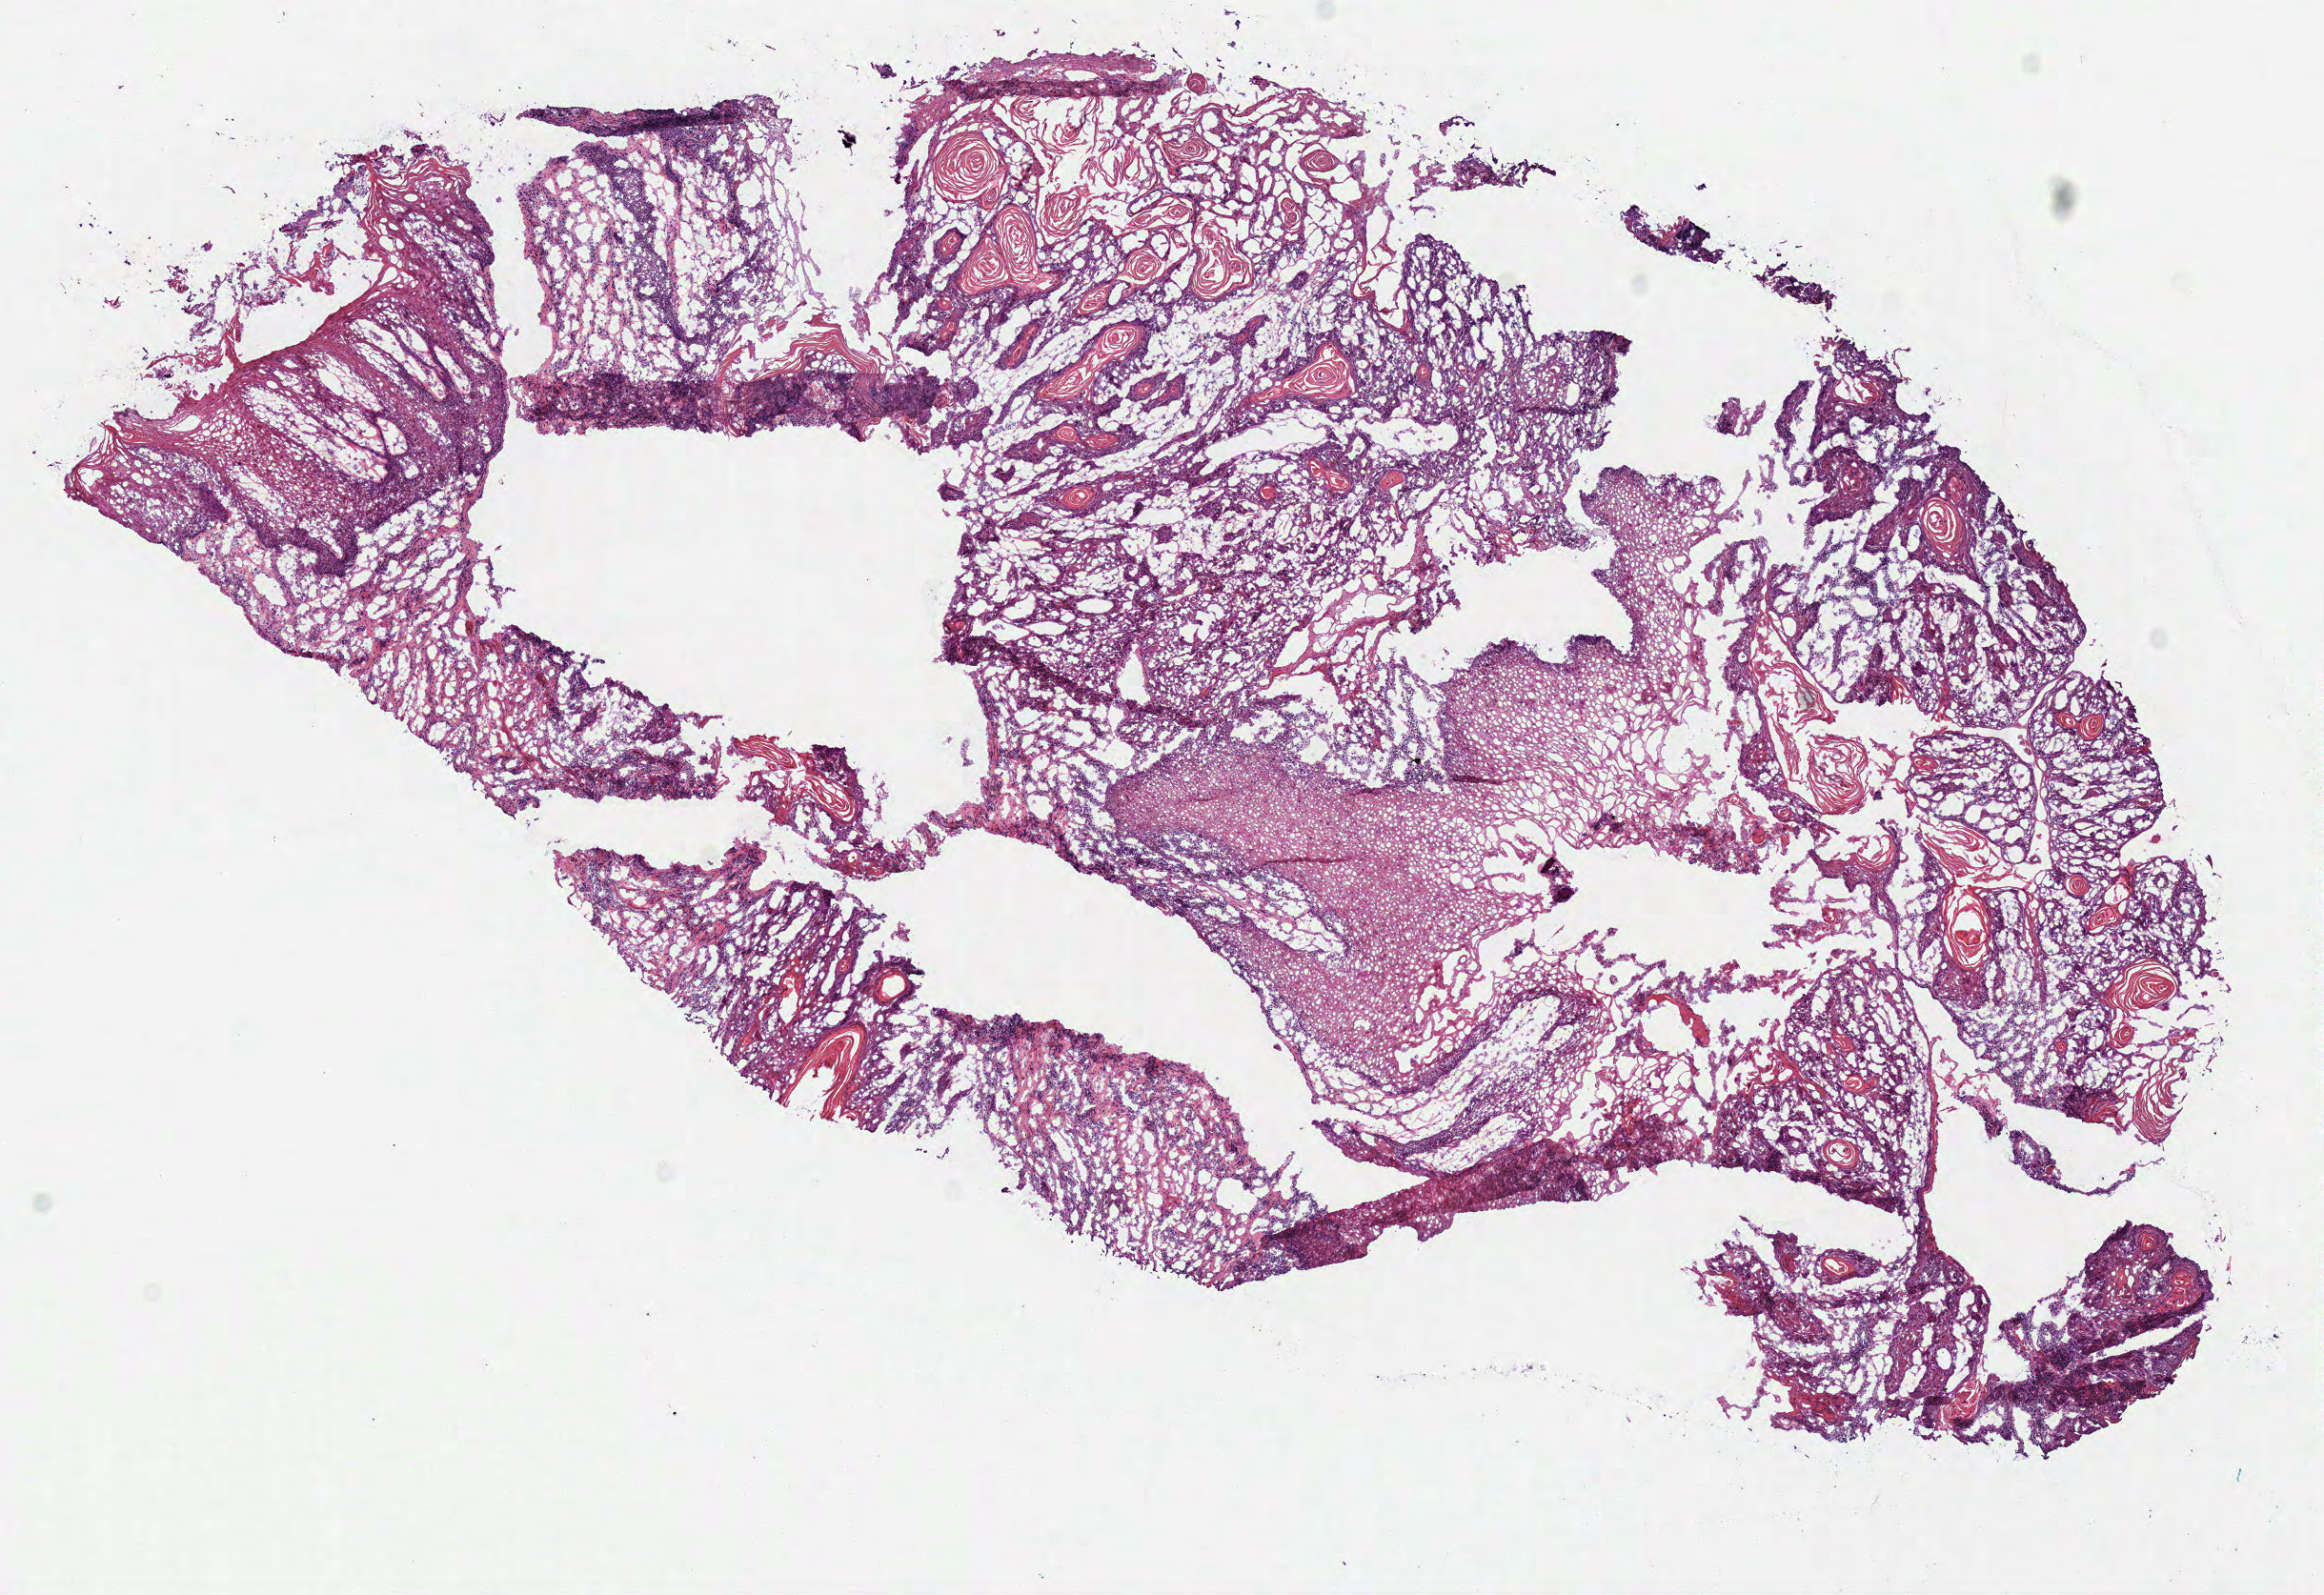
H&E whole-slide image — low-resolution overview of the scanned area, about 9.6 x 6.6 mm (acquisition: 40x scan); frozen section from the top of the tissue portion; head and neck, primary tumour sample. Patient: male, age at initial diagnosis 34 years. Histologic grade: G2 (moderately differentiated). Composition of this section per pathologist review: tumour cells 85%, tumour nuclei 80%, normal cells 0%, stromal cells 14%, necrosis 1%. Inflammatory infiltration, as recorded: lymphocyte infiltration 9%, monocyte infiltration 1%, neutrophil infiltration 0%.
- diagnosis: Squamous cell carcinoma, NOS
- AJCC pathologic stage: II